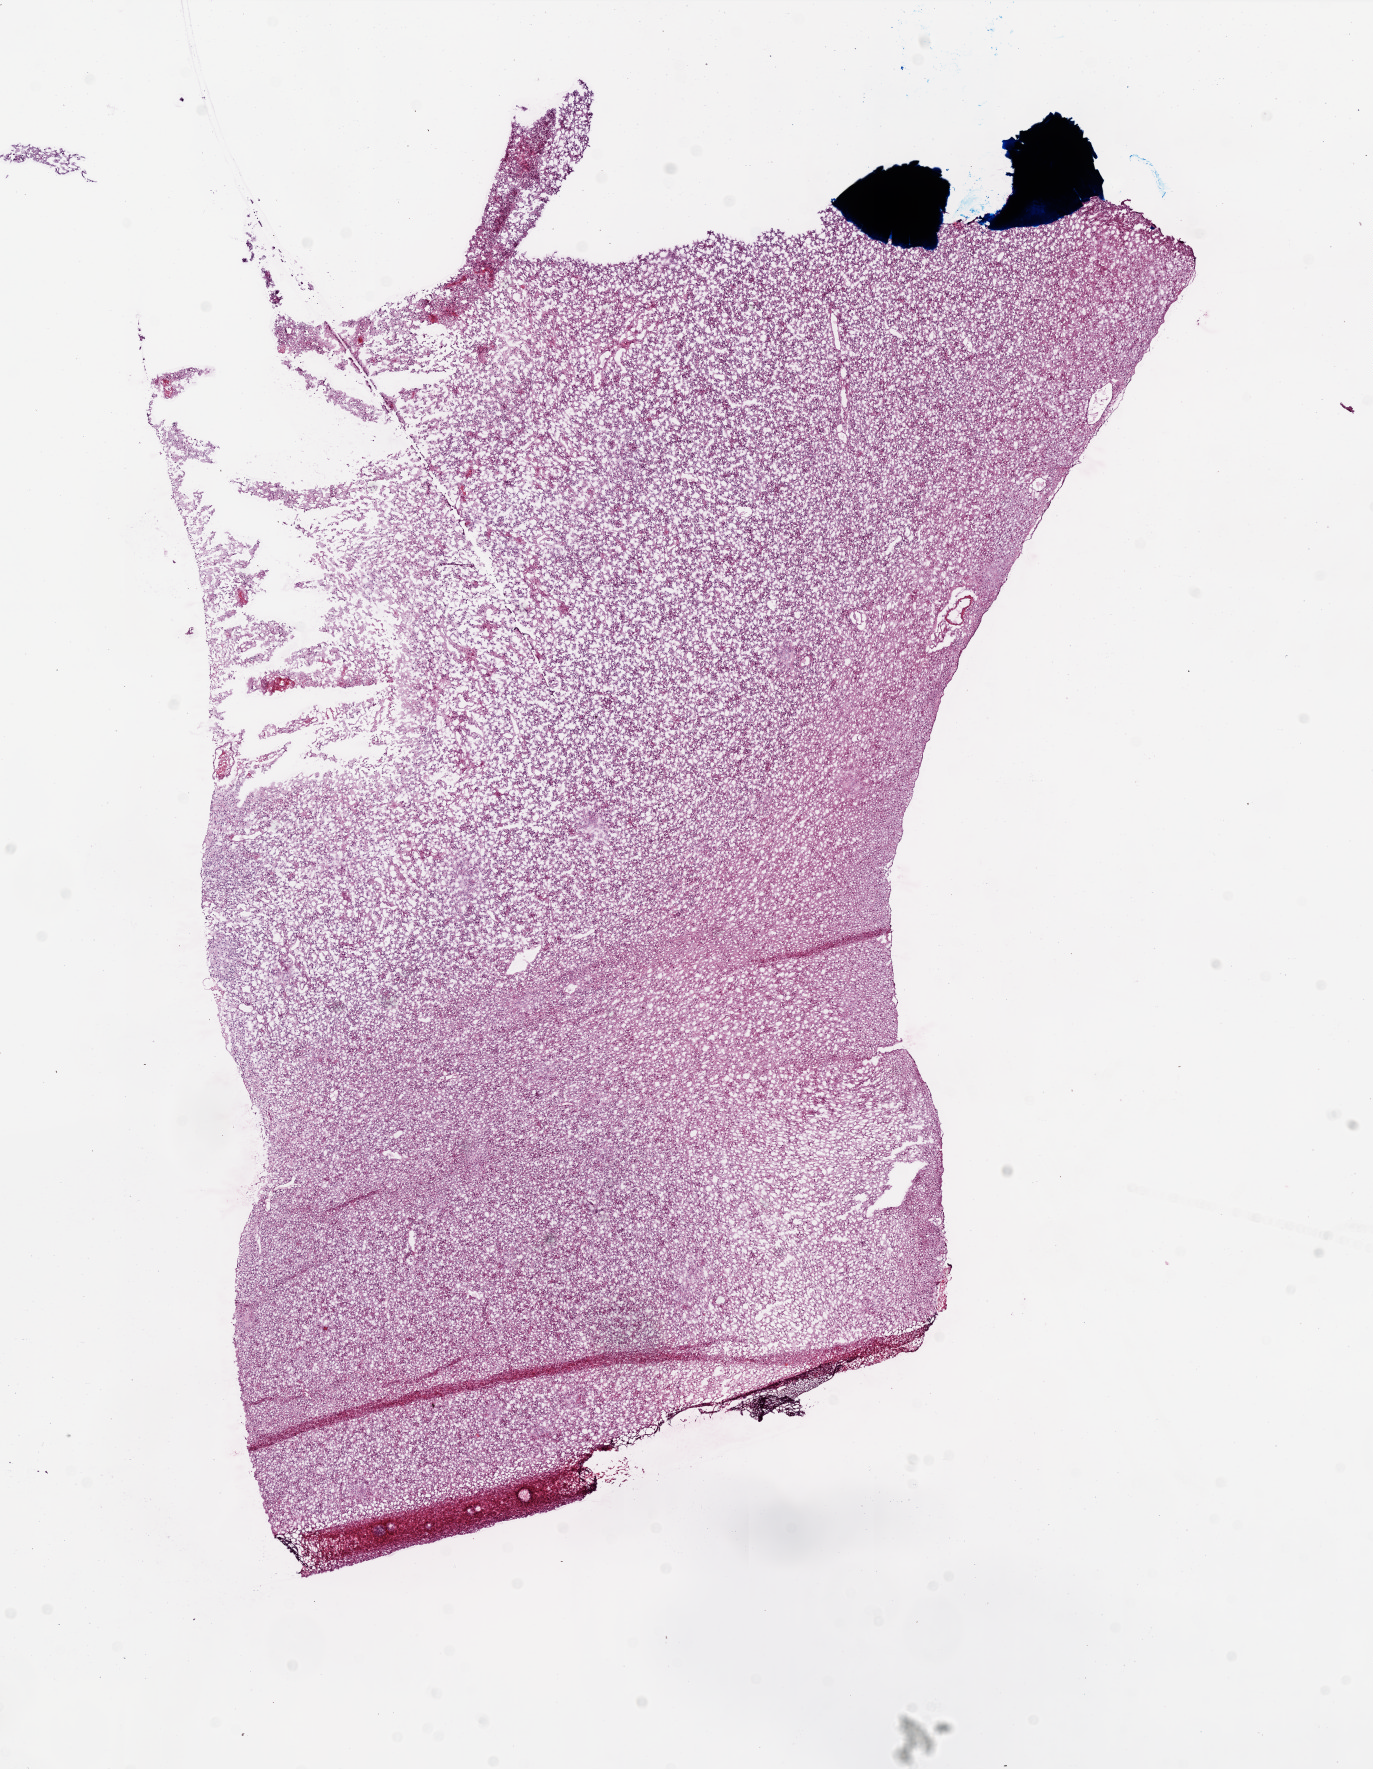
Digitized Hematoxylin and eosin (H&E) stained tissue section (whole slide), low-resolution overview of the scanned area, about 11.0 x 14.2 mm, frozen section from the top of the tissue portion, sample: primary tumour, brain. Male patient; age at initial diagnosis 68 years. Composition of this section per pathologist review: tumour cells 95%, tumour nuclei 100%, normal cells 0%, stromal cells 0%, necrosis 5%. Inflammatory infiltration, as recorded: lymphocyte infiltration 0%.
• histologic diagnosis: Glioblastoma